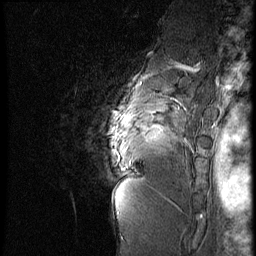
Breast MRI (dynamic contrast-enhanced), one sagittal slice. Position 54 of 60 along the scan axis. 4 images stored at this slice position (order not interpretable as contrast timing). 1.5 T. TE 4.2 ms, TR 9 ms. 2.5 mm slice thickness. 256 × 256 image matrix, field of view 180 × 180 mm. Patient: female, 56 years. From the clinical record (not read from this slice): setting: breast cancer imaged before/during neoadjuvant chemotherapy; receptor status: HER2-positive.
Outlined on this slice (semi-automatically segmented with operator editing):
- analysis volume of interest (the breast-tissue region the enhancement analysis was run in; not a lesion): box from (x=88, y=83) to (x=199, y=177) px
- tumour enhancement mask (voxels above the 140 % enhancement threshold inside the analysis volume of interest): (x=116, y=134)–(x=119, y=136)